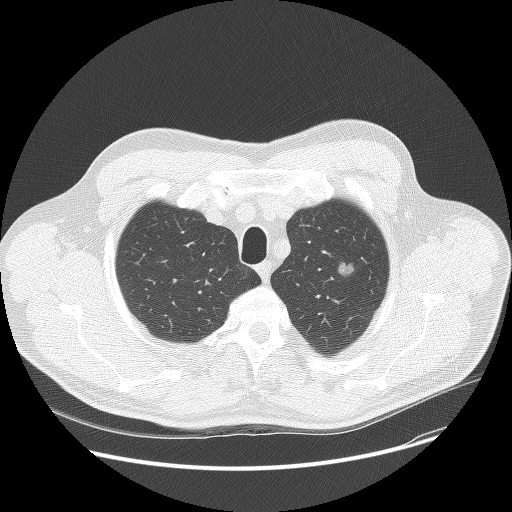
Chest CT (low-dose screening protocol), one axial image; baseline annual screen; lung window (W 1500 / L -600 HU); lung (sharp) reconstruction kernel (BONE); slice 20 of 132 in the series. Male, age 60 years at enrolment. Former smoker at enrolment.
Lesion marked by an expert reader, bounding box <322,248,370,291> (left, top, right, bottom; pixels). The screening reader recorded 2 non-calcified nodules or masses ≥4 mm on this exam (left upper lobe, right lower lobe); which of them this box marks is not recorded. Official screen result: positive, change unspecified: nodule(s) >= 4 mm or enlarging nodule(s), mass(es), or other non-specific abnormalities suspicious for lung cancer. Later outcome: lung cancer diagnosed 784 days after this screen — bronchiolo-alveolar carcinoma, non-mucinous, left upper lobe, well differentiated (G1), stage IA (AJCC 6th edition), 16 mm at pathology.